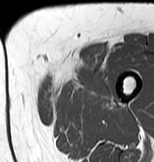
MRI of an extremity soft-tissue mass, one axial slice. Slice 12 of 83 in the series (ordered by position). MR volume resampled by the dataset authors to the PET/CT grid (not the native acquisition matrix). 3.27 mm slice thickness. 154 × 162 image matrix, field of view 150 × 158 mm. Female patient. Case-level facts recorded for this patient, not image findings: histological type: myxofibrosarcoma; grade: intermediate; site of the primary tumour: left thigh.
Structures marked on this image (expert contour drawn on MRI and transferred to this co-registered scan by the dataset authors):
- gross tumour volume including surrounding oedema: bounding box (x1, y1, x2, y2) in pixels: (40, 66, 114, 106)